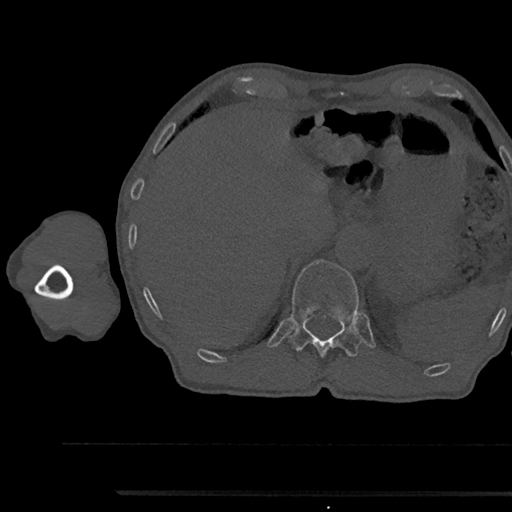
CT including the spine, one axial slice. Position 719 of 797 along the scan axis. Reconstruction kernel Br40s/3. Bone window (W 1800 / L 400 HU). 0.5 mm slice thickness. 512 × 512 image matrix, field of view 367 × 367 mm. Male patient, age 79 years. From the clinical record (not read from this slice): primary cancer: prostate.
Annotated regions visible in this slice (semi-automatic segmentation, software-assisted and operator-edited):
- T12 vertebra: box from (x=290, y=259) to (x=361, y=358) px